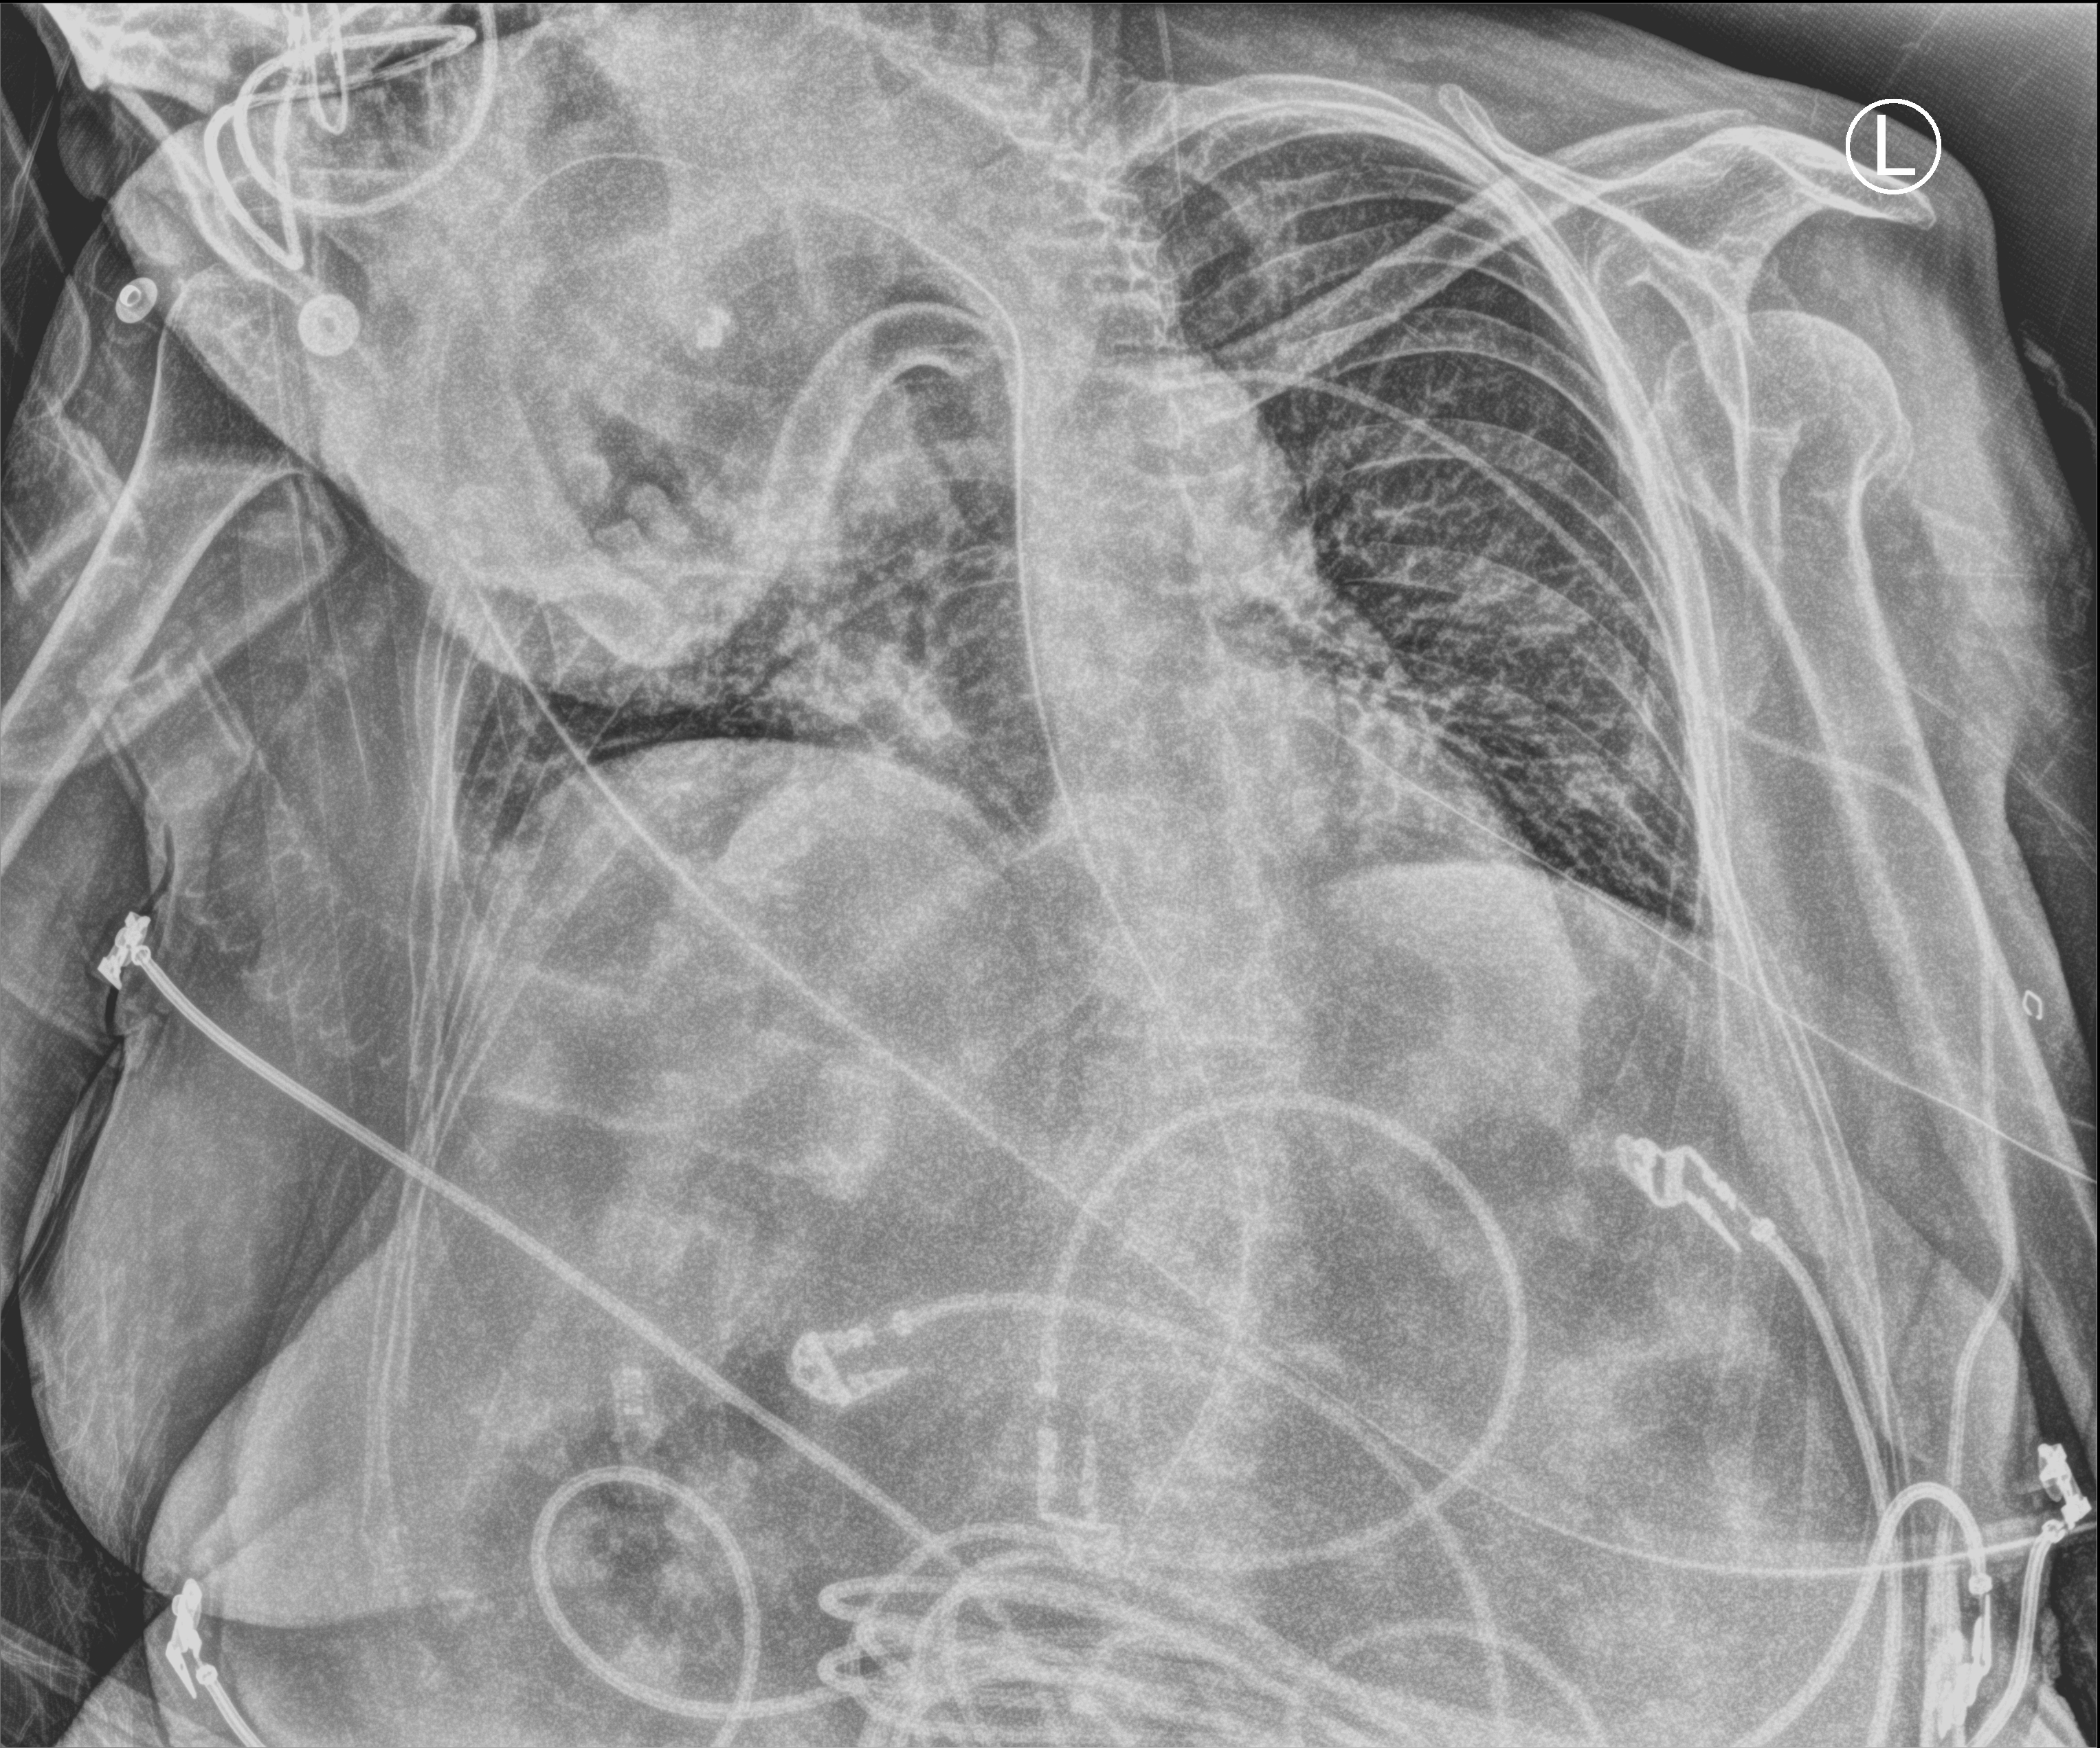
Portable chest radiograph, anteroposterior (AP) projection. Patient hospitalised with COVID-19; female, aged 75–90 years.
Hospital-stay facts (about this admission, not read from this image; timing relative to this image not recorded): other chronic lung disease (admission record): yes.